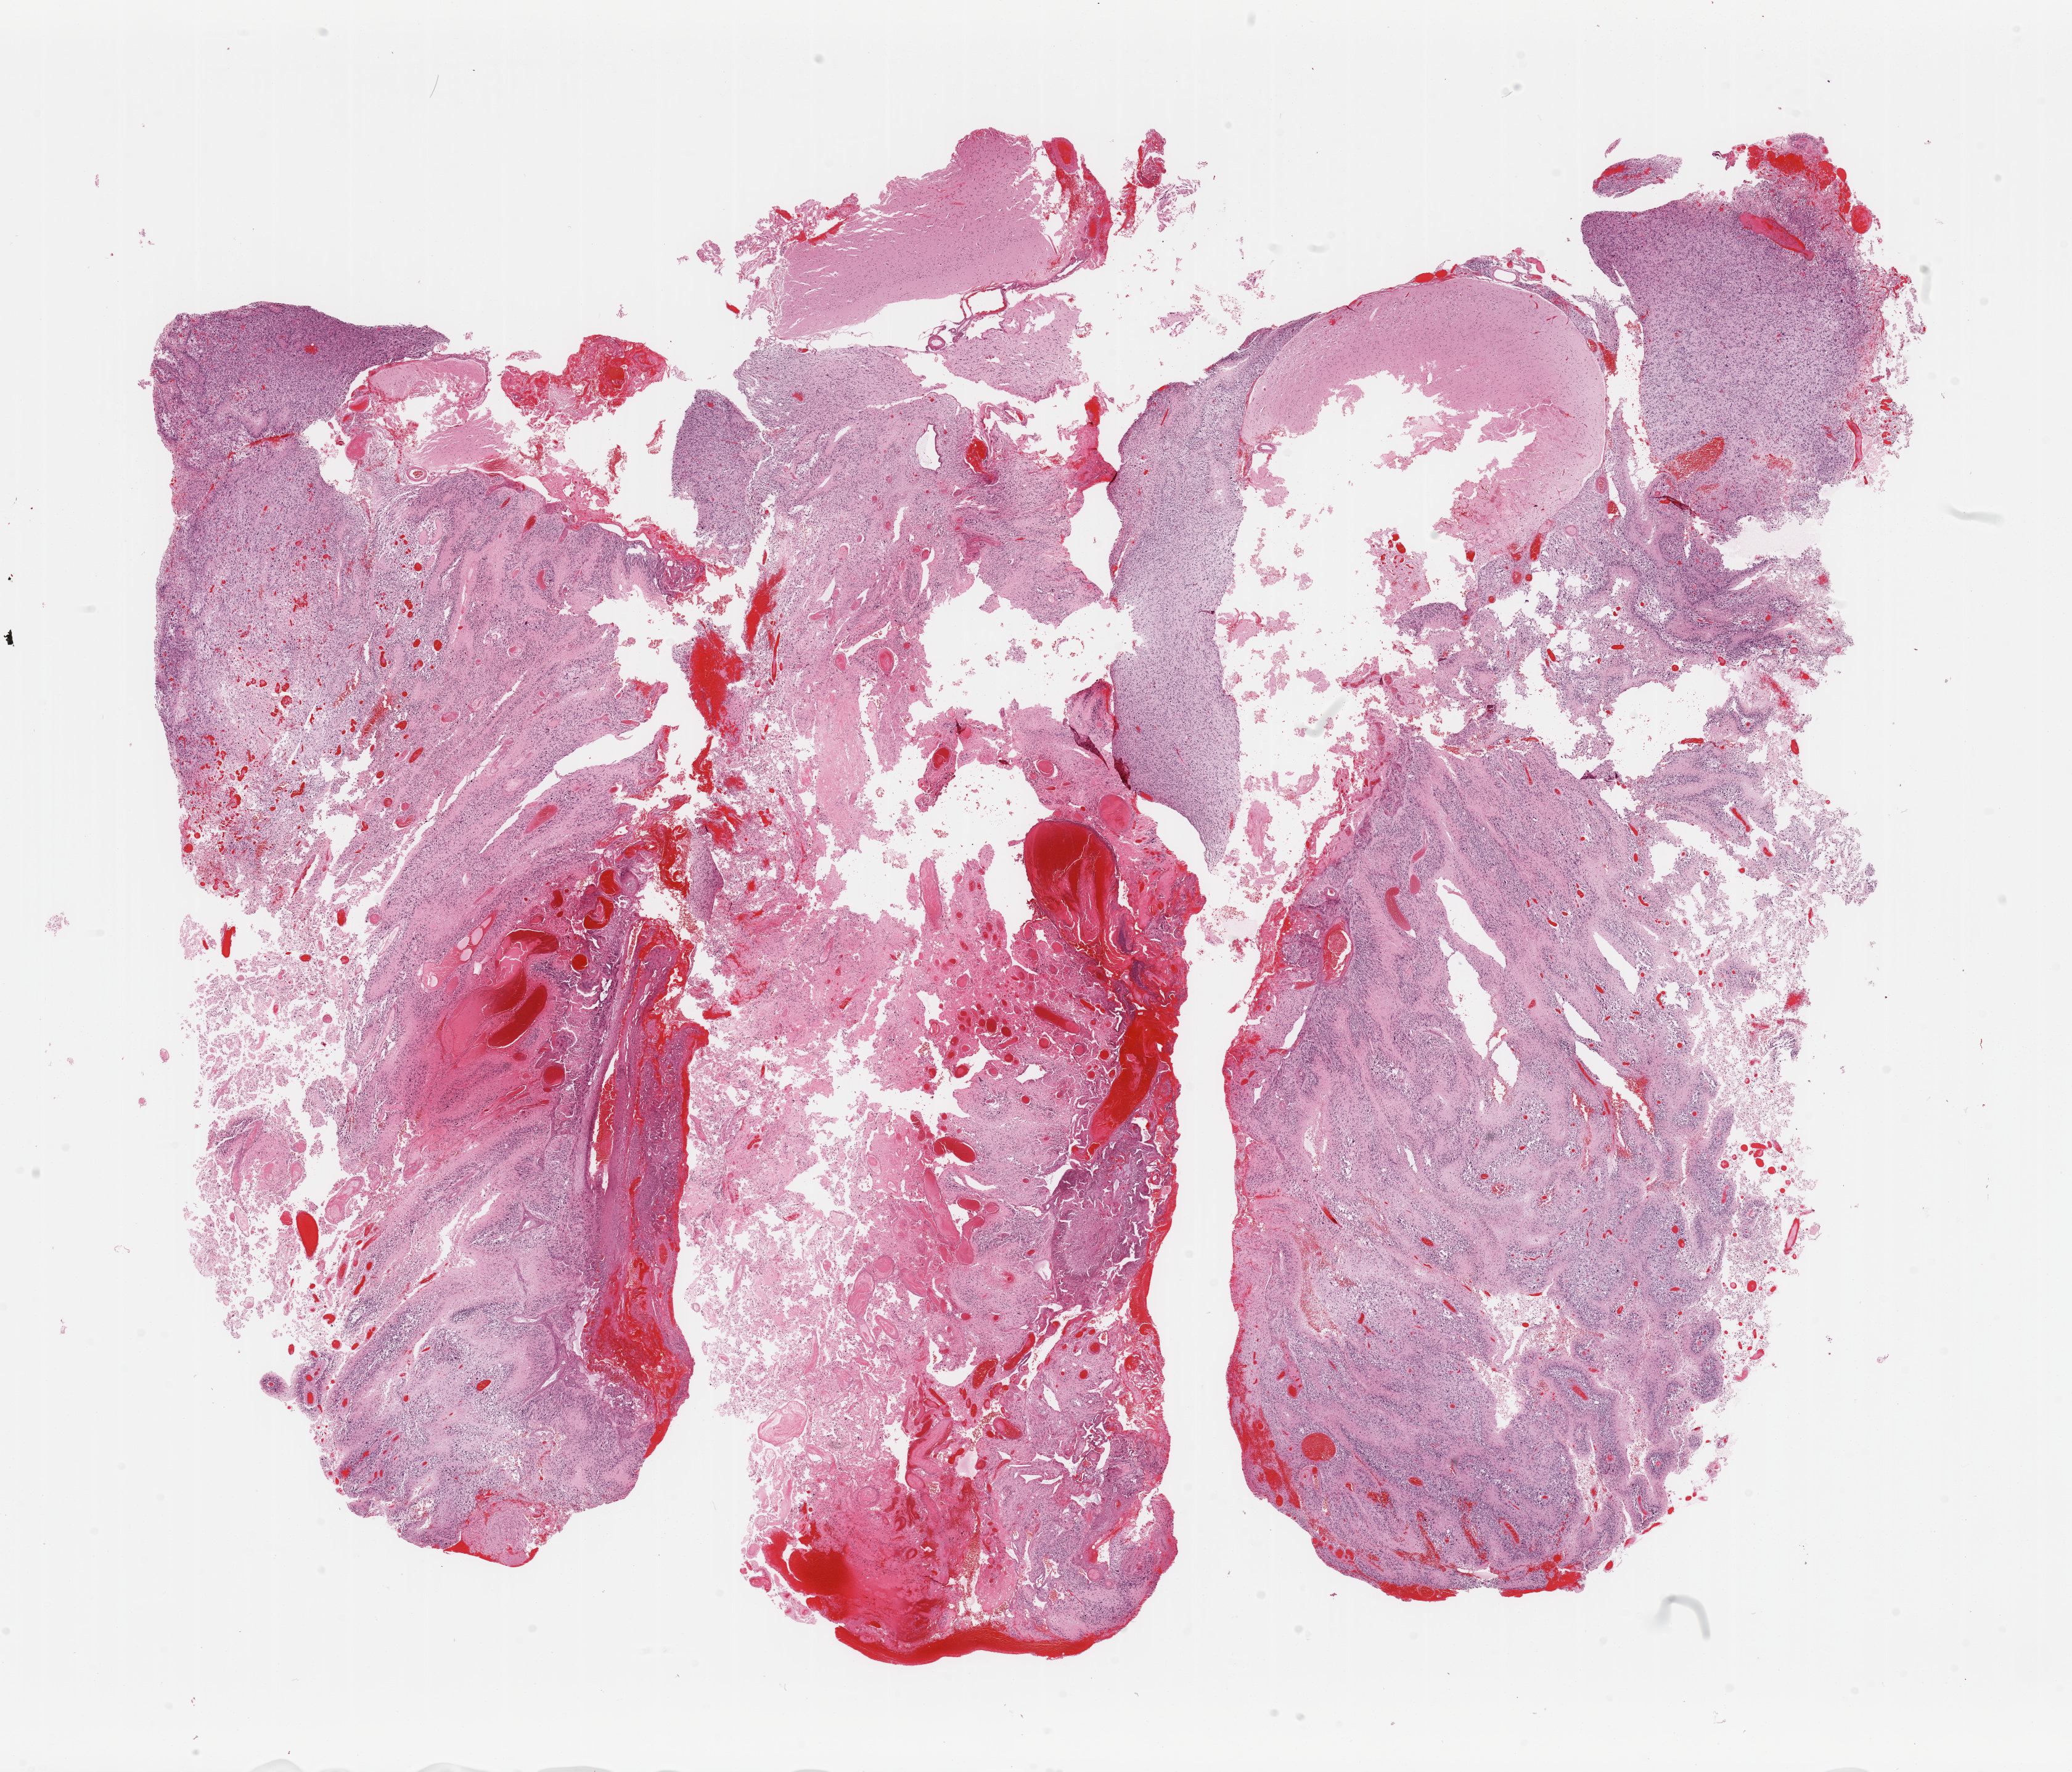
Whole-slide histology image, H&E — whole scanned area (about 26.6 x 22.7 mm, acquisition: 20x scan) shown as a low-resolution overview. Tumour tissue sample, brain. 58-year-old male patient.
Diagnosis: Glioblastoma. Primary tumour site (as recorded): temporal lobe.